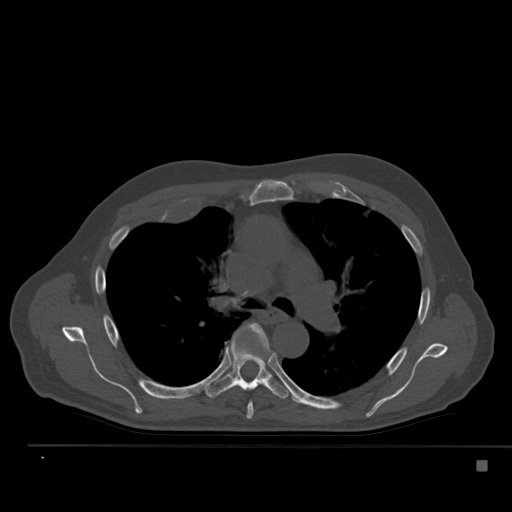
CT including the spine, one axial slice; slice 354 of 517 in the series (ordered by position); 120 kVp; bone window (W 1800 / L 400 HU); 1.5 mm slice thickness; 512 × 512 image matrix, field of view 408 × 408 mm. Patient: male, 70 years. From the clinical record (not read from this slice): primary cancer: renal; vertebrae with lytic lesions (as recorded): T4, T6, T10, T12, L3, L4, L5.
Annotated regions visible in this slice (semi-automatic segmentation, software-assisted and operator-edited):
- T5 vertebra: box from (x=246, y=323) to (x=272, y=419) px
- T6 vertebra: (x=206, y=331)–(x=292, y=399)